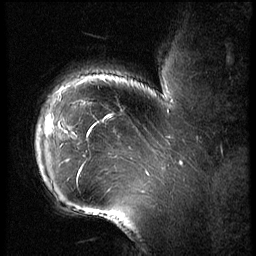
Breast MRI (dynamic contrast-enhanced), one sagittal slice. Slice 51 of 62 in the series (ordered by position). 3 images stored at this slice position (order not interpretable as contrast timing). 1.5 T. TE 4.2 ms, TR 9 ms. 2.5 mm slice thickness. 256 × 256 image matrix, field of view 180 × 180 mm. Female patient, age 43 years. Case-level facts recorded for this patient, not image findings: setting: breast cancer imaged before/during neoadjuvant chemotherapy; receptor status: HER2-positive.
Outlined on this slice (semi-automatically segmented with operator editing):
- analysis volume of interest (the breast-tissue region the enhancement analysis was run in; not a lesion): bounding box [x1, y1, x2, y2] px = [36, 90, 82, 203]
- tumour enhancement mask (voxels above the 140 % enhancement threshold inside the analysis volume of interest): [50, 118, 54, 126]